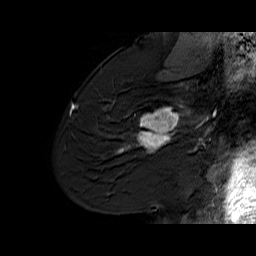
Breast MRI (dynamic contrast-enhanced), one sagittal slice; position 41 of 60 along the scan axis; dynamic contrast-enhanced series, time point 2 of 6 at this slice position (early post-contrast); 1.5 T; TE 6.1 ms, TR 32.9 ms; 256 × 256 image matrix, field of view 220 × 220 mm. Female patient. Case-level facts recorded for this patient, not image findings: setting: breast cancer imaged before/during neoadjuvant chemotherapy; receptor status: HER2-positive.
Structures marked on this image (semi-automatically segmented with operator editing):
- analysis volume of interest (the breast-tissue region the enhancement analysis was run in; not a lesion): bounding box <127,96,194,165> (left, top, right, bottom; pixels)
- tumour enhancement mask (voxels above the 100 % enhancement threshold inside the analysis volume of interest): <127,107,187,152>